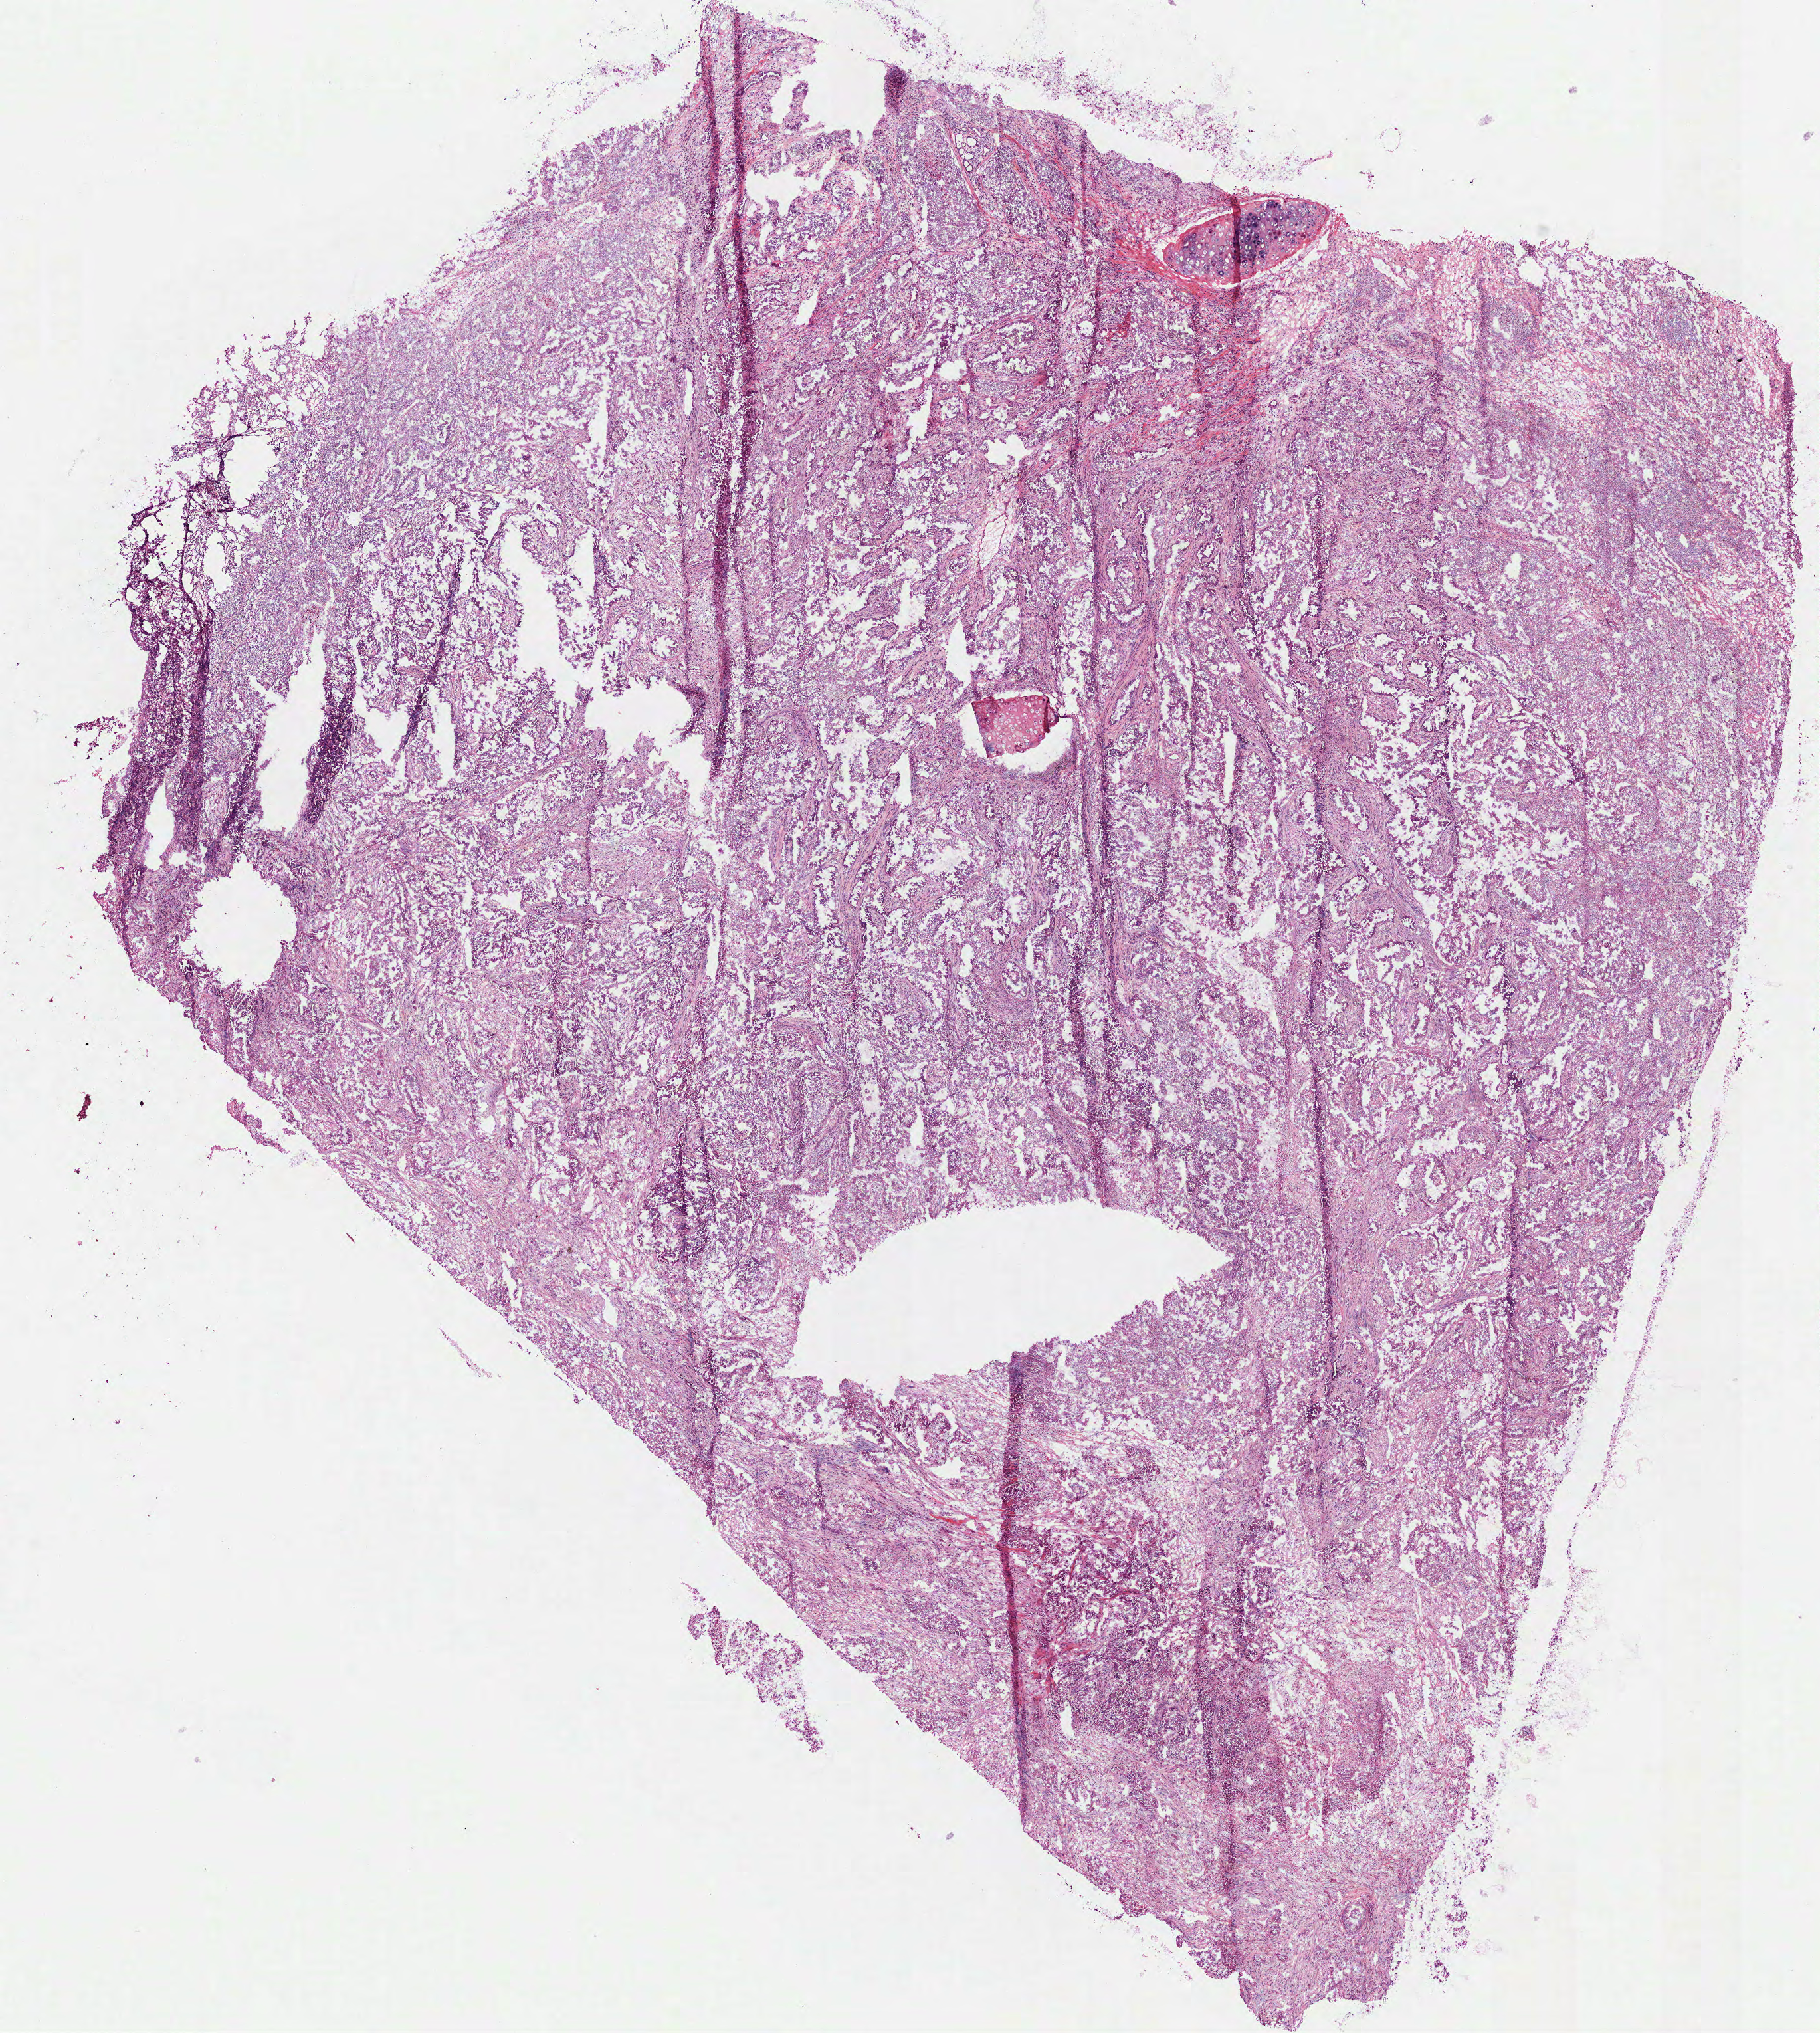
Whole-slide histology image, Hematoxylin and eosin (H&E) stained — whole scanned area (about 11.0 x 12.3 mm, acquisition: 40x scan) shown as a low-resolution overview, frozen section, sample: primary tumour, lung. Female, age 60 years at initial diagnosis. Pathologist review of this section (percent, as recorded): tumour cells 80%, tumour nuclei 75%, normal cells 5%, stromal cells 15%, necrosis 0%.
- laterality: left
- AJCC pathologic stage: IB (7th edition)
- pathologic diagnosis: Adenocarcinoma, NOS (upper lobe, lung)
- TNM: T2 N0 M0